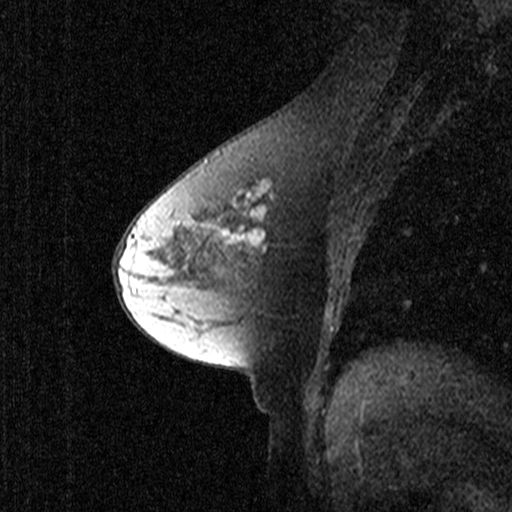
Breast MRI (dynamic contrast-enhanced), one sagittal slice. Slice 23 of 44 in the series (ordered by position). Dynamic contrast-enhanced study with each time point stored as its own series, time point 2 of 3 at this slice position (early post-contrast, ordered by acquisition time). 1.5 T. TE 4.5 ms, TR 11 ms. 512 × 512 image matrix, field of view 200 × 200 mm. Female patient, age 53 years. From the clinical record (not read from this slice): setting: breast cancer imaged before/during neoadjuvant chemotherapy; receptor status: HR-positive, HER2-negative.
Structures marked on this image (semi-automatically segmented with operator editing):
- analysis volume of interest (the breast-tissue region the enhancement analysis was run in; not a lesion): bounding box <192,146,303,281> (left, top, right, bottom; pixels)
- tumour enhancement mask (voxels above the 90 % enhancement threshold inside the analysis volume of interest): <232,182,269,246>